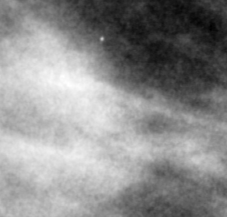
Crop from a digitized film mammogram around one marked abnormality; right breast; MLO view.
Finding: mass, shape lobulated, margins obscured; BI-RADS assessment category 3; pathology result (as recorded, not read from the image): benign.